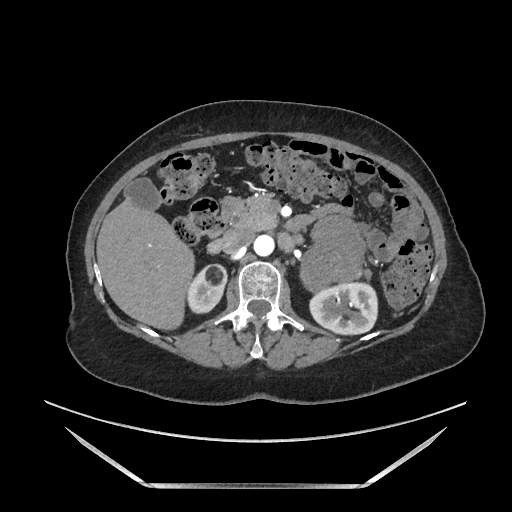
Contrast-enhanced abdominal CT, one axial slice; soft-tissue window (W 400 / L 40 HU); 1.25 mm slice thickness; 512 × 512 image matrix, field of view 440 × 440 mm. Female patient. Case-level facts recorded for this patient, not image findings: diagnosis: adrenocortical carcinoma; tumour side: left adrenal; tumour size at pathology: 12.5 cm; Ki-67 index: 39 %; stage (as recorded): 3.
Structures marked on this image (semi-automatically segmented with operator editing):
- mass: box from (x=302, y=217) to (x=363, y=289) px